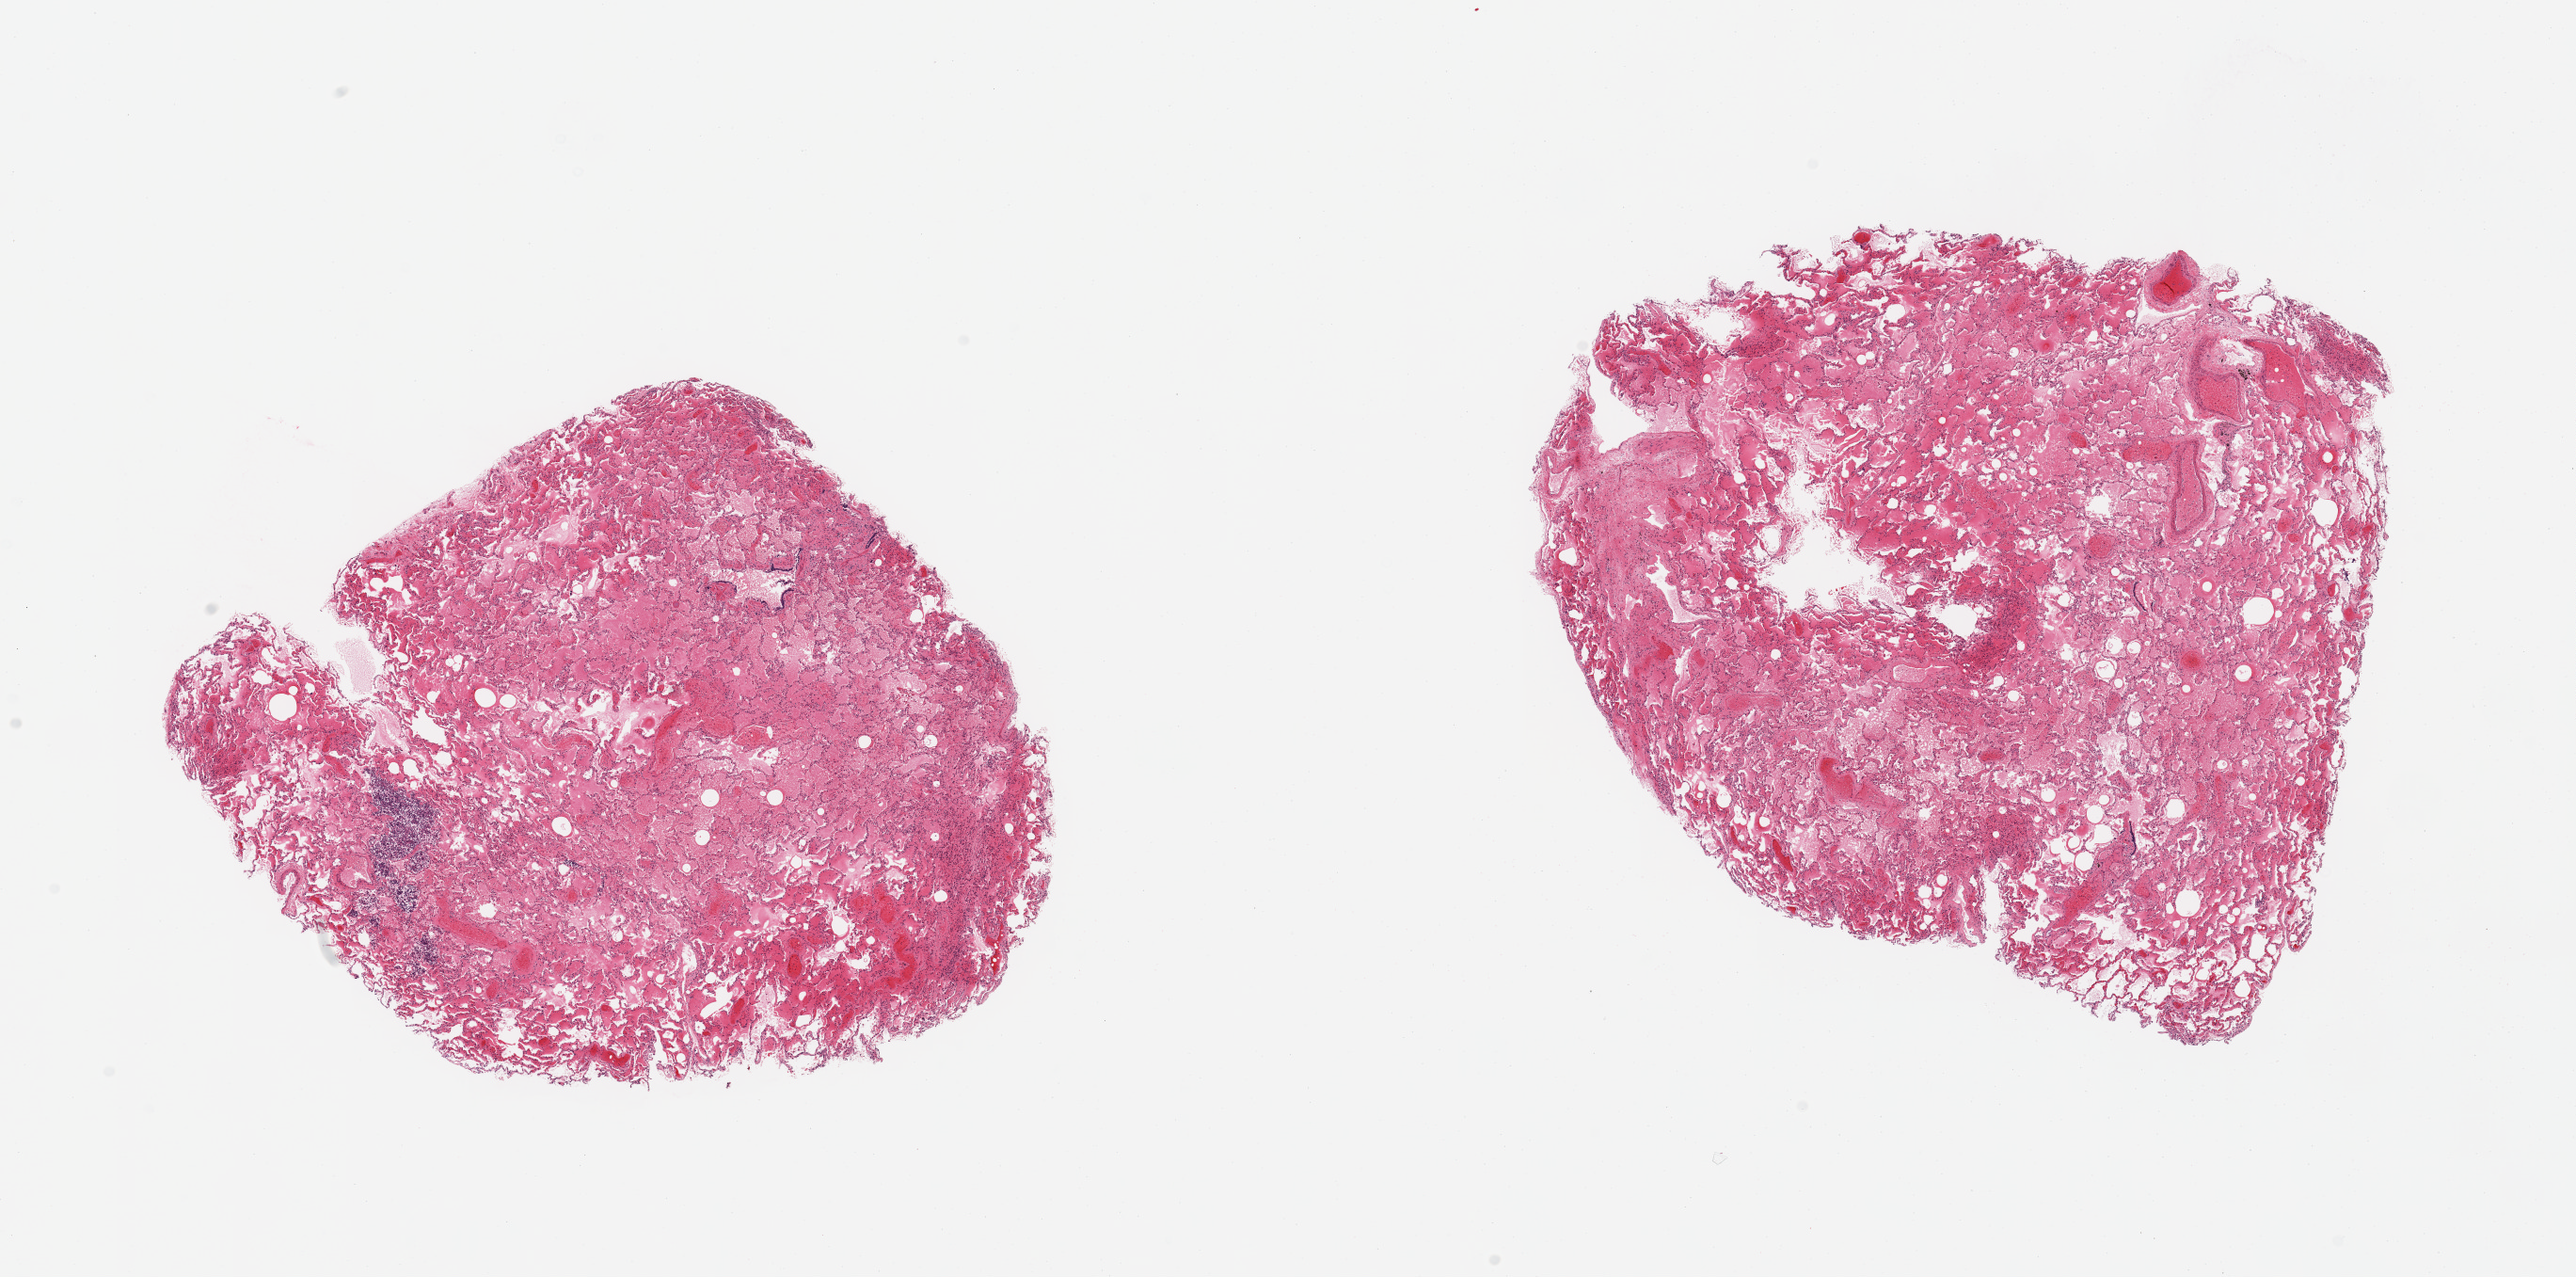
Whole-slide image, hematoxylin and eosin (H&E) stain, brightfield, low-resolution overview of the scanned area, about 21.7 x 10.7 mm (acquisition: 20x scan). PAXgene-fixed, paraffin-embedded tissue. Section of lung (target tissue). Donor tissue sample. Female donor.
Review note (as recorded): 2 pieces; extensive pulmonary edema & hemorrhage; focal collection of bronchial cells in air spaces.